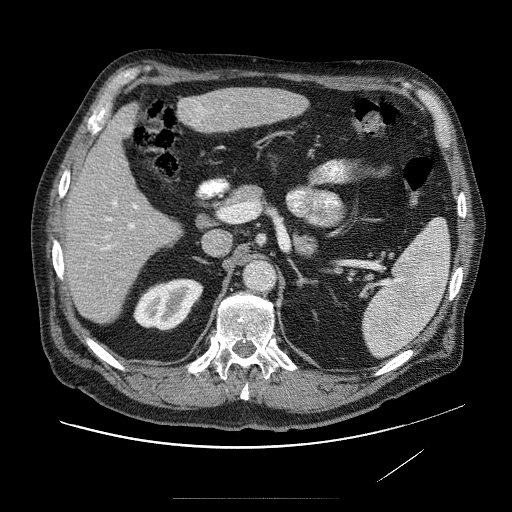
Contrast-enhanced abdominal CT (liver protocol), one axial slice; slice 37 of 89 in the series (ordered by position); reconstruction kernel STANDARD; soft-tissue window (W 400 / L 40 HU); 2.5 mm slice thickness; 512 × 512 image matrix, field of view 420 × 420 mm. From the clinical record (not read from this slice): diagnosis: hepatocellular carcinoma (patient treated with transarterial chemoembolisation; whether this scan precedes or follows treatment is not stated here); TNM stage (as recorded): Stage-IVA; Child-Pugh class: A.
Structures marked on this image (semi-automatic segmentation, software-assisted and operator-edited):
- liver parenchyma outside the tumour (the mass and vessels are separate outlines, so this box may not span the whole liver): box from (x=62, y=84) to (x=314, y=326) px
- mass: (x=181, y=95)–(x=212, y=126)
- liver vessels: (x=88, y=119)–(x=244, y=284)